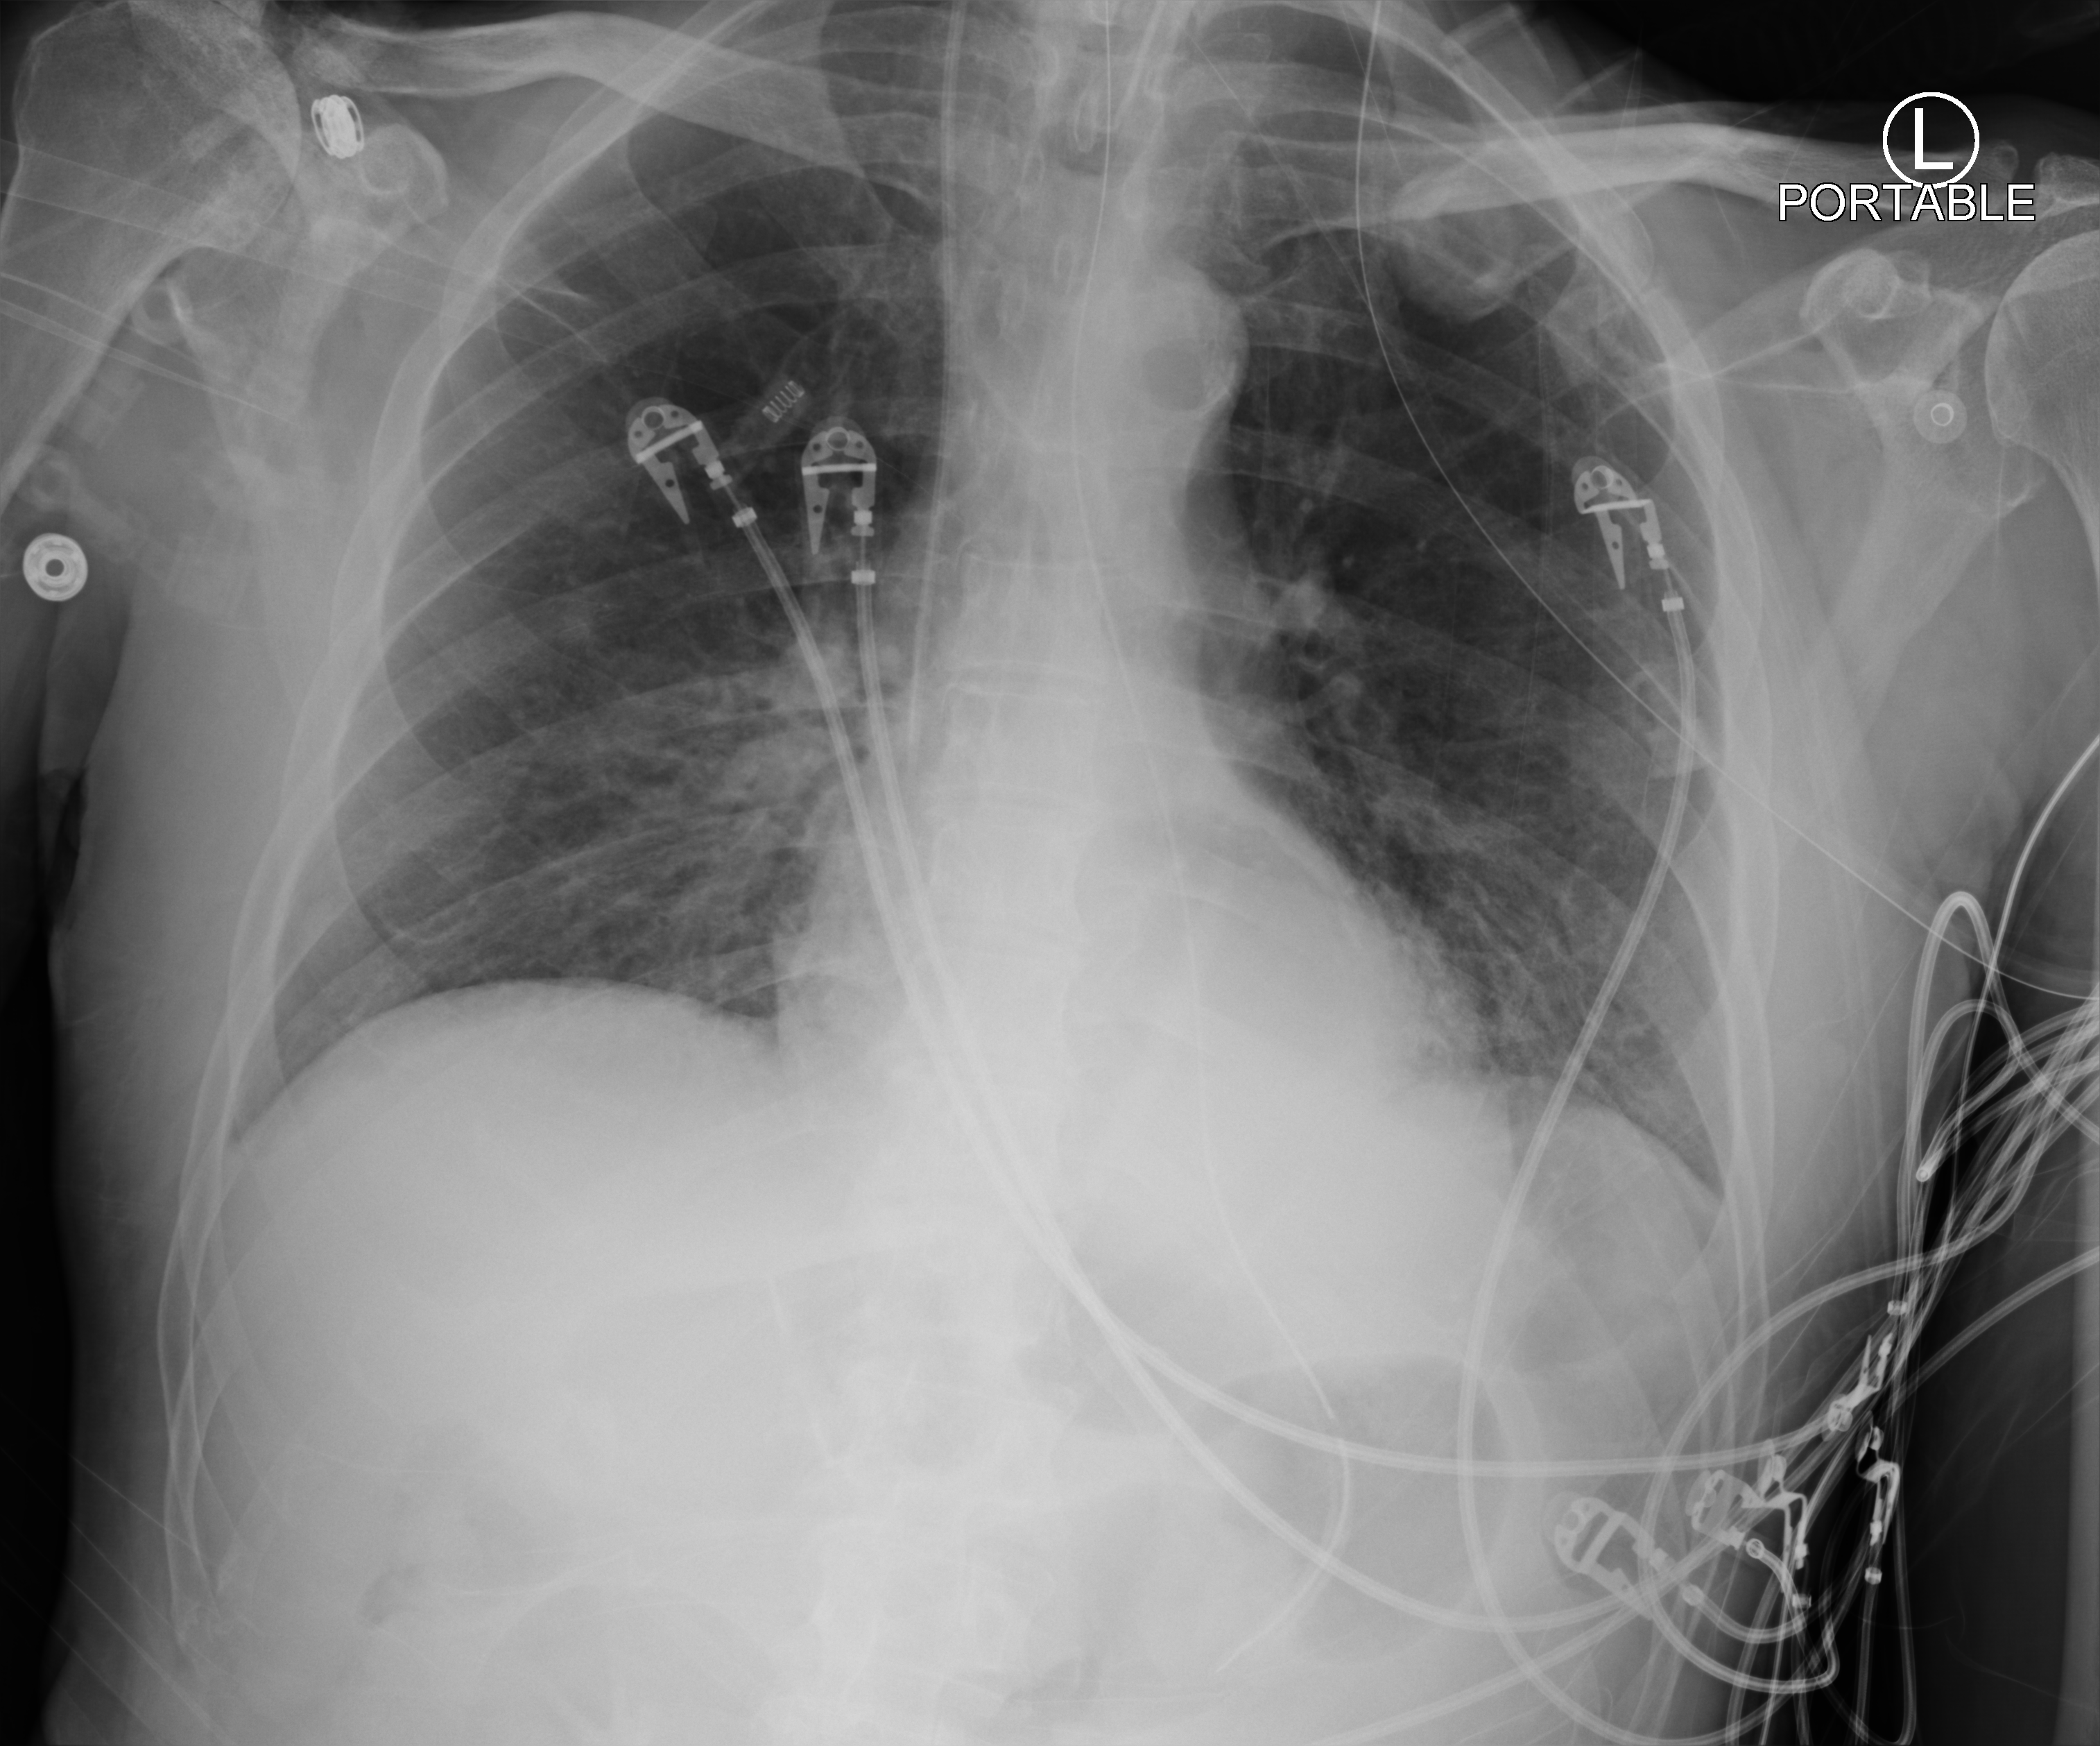
Portable chest radiograph; anteroposterior (AP) projection. Male patient hospitalised with COVID-19, age 75–90 years.
Admission-level facts for this patient (not findings on this image; timing relative to this image not recorded):
- admitted to intensive care during this hospital stay: yes